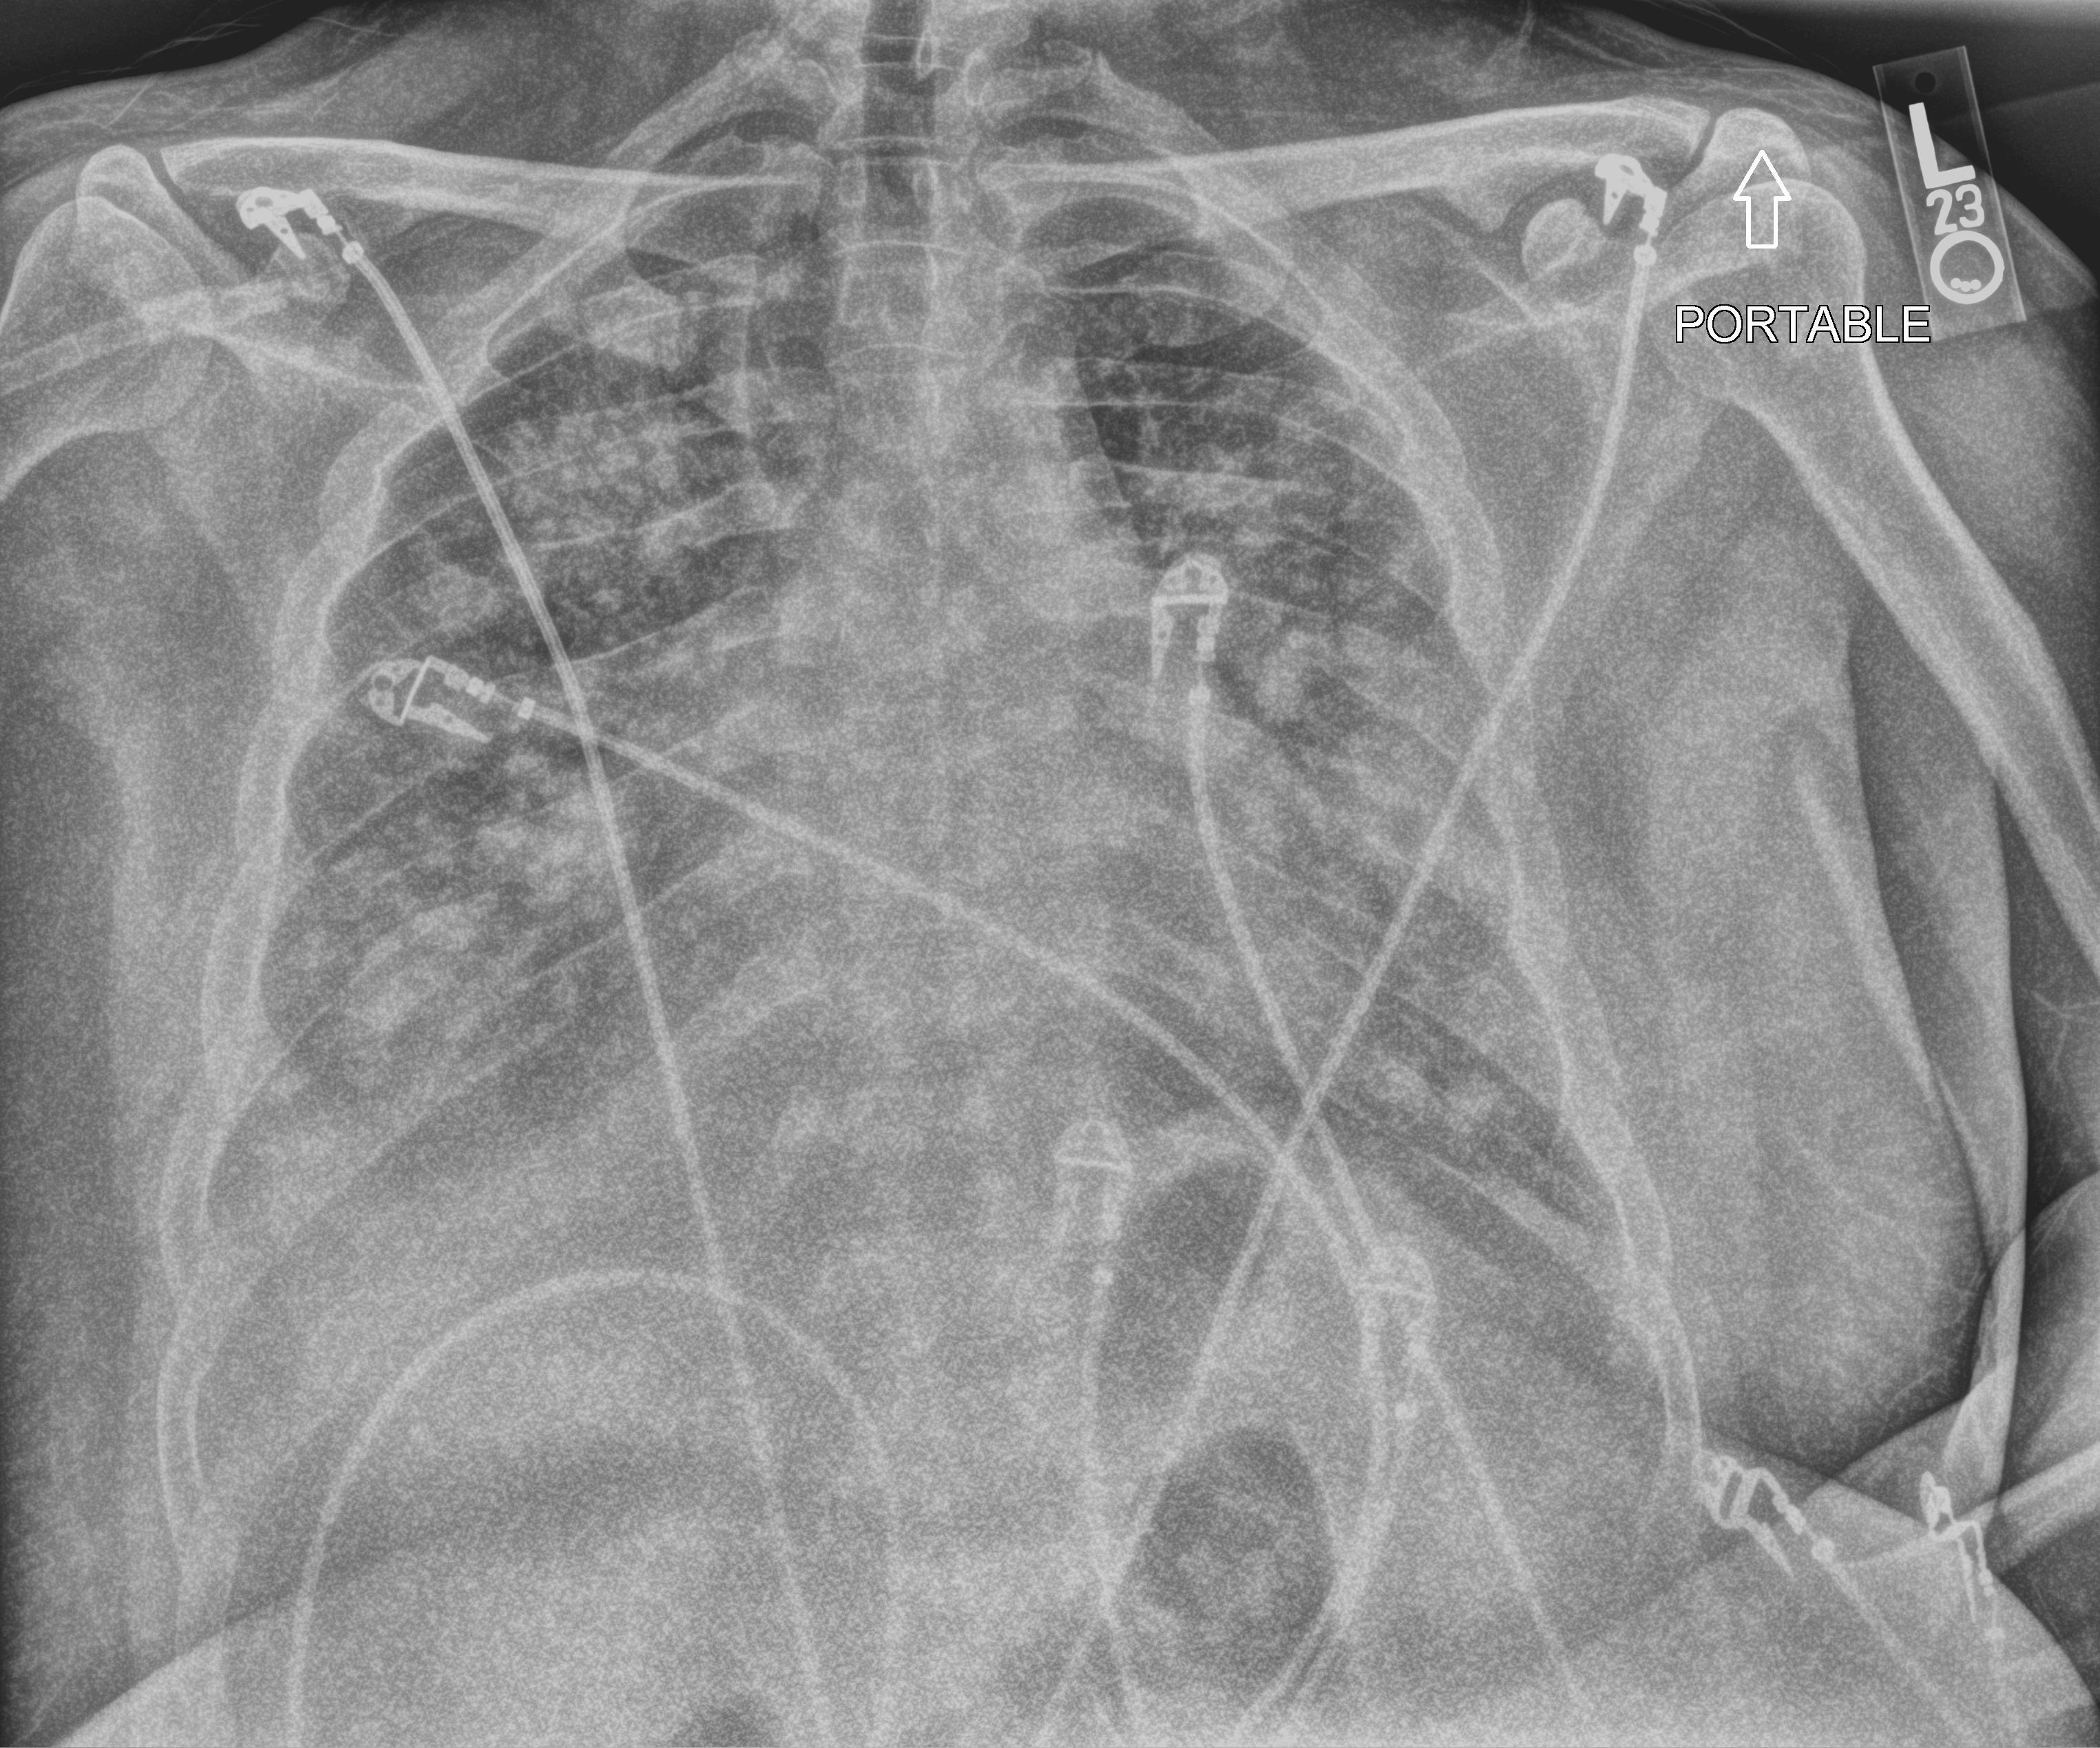
Bedside chest radiograph (computed radiography); anteroposterior (AP) projection. Adult patient hospitalised with COVID-19, age 18–59 years.
Hospital-stay facts (about this admission, not read from this image; timing relative to this image not recorded): mechanically ventilated during this hospital stay: yes.